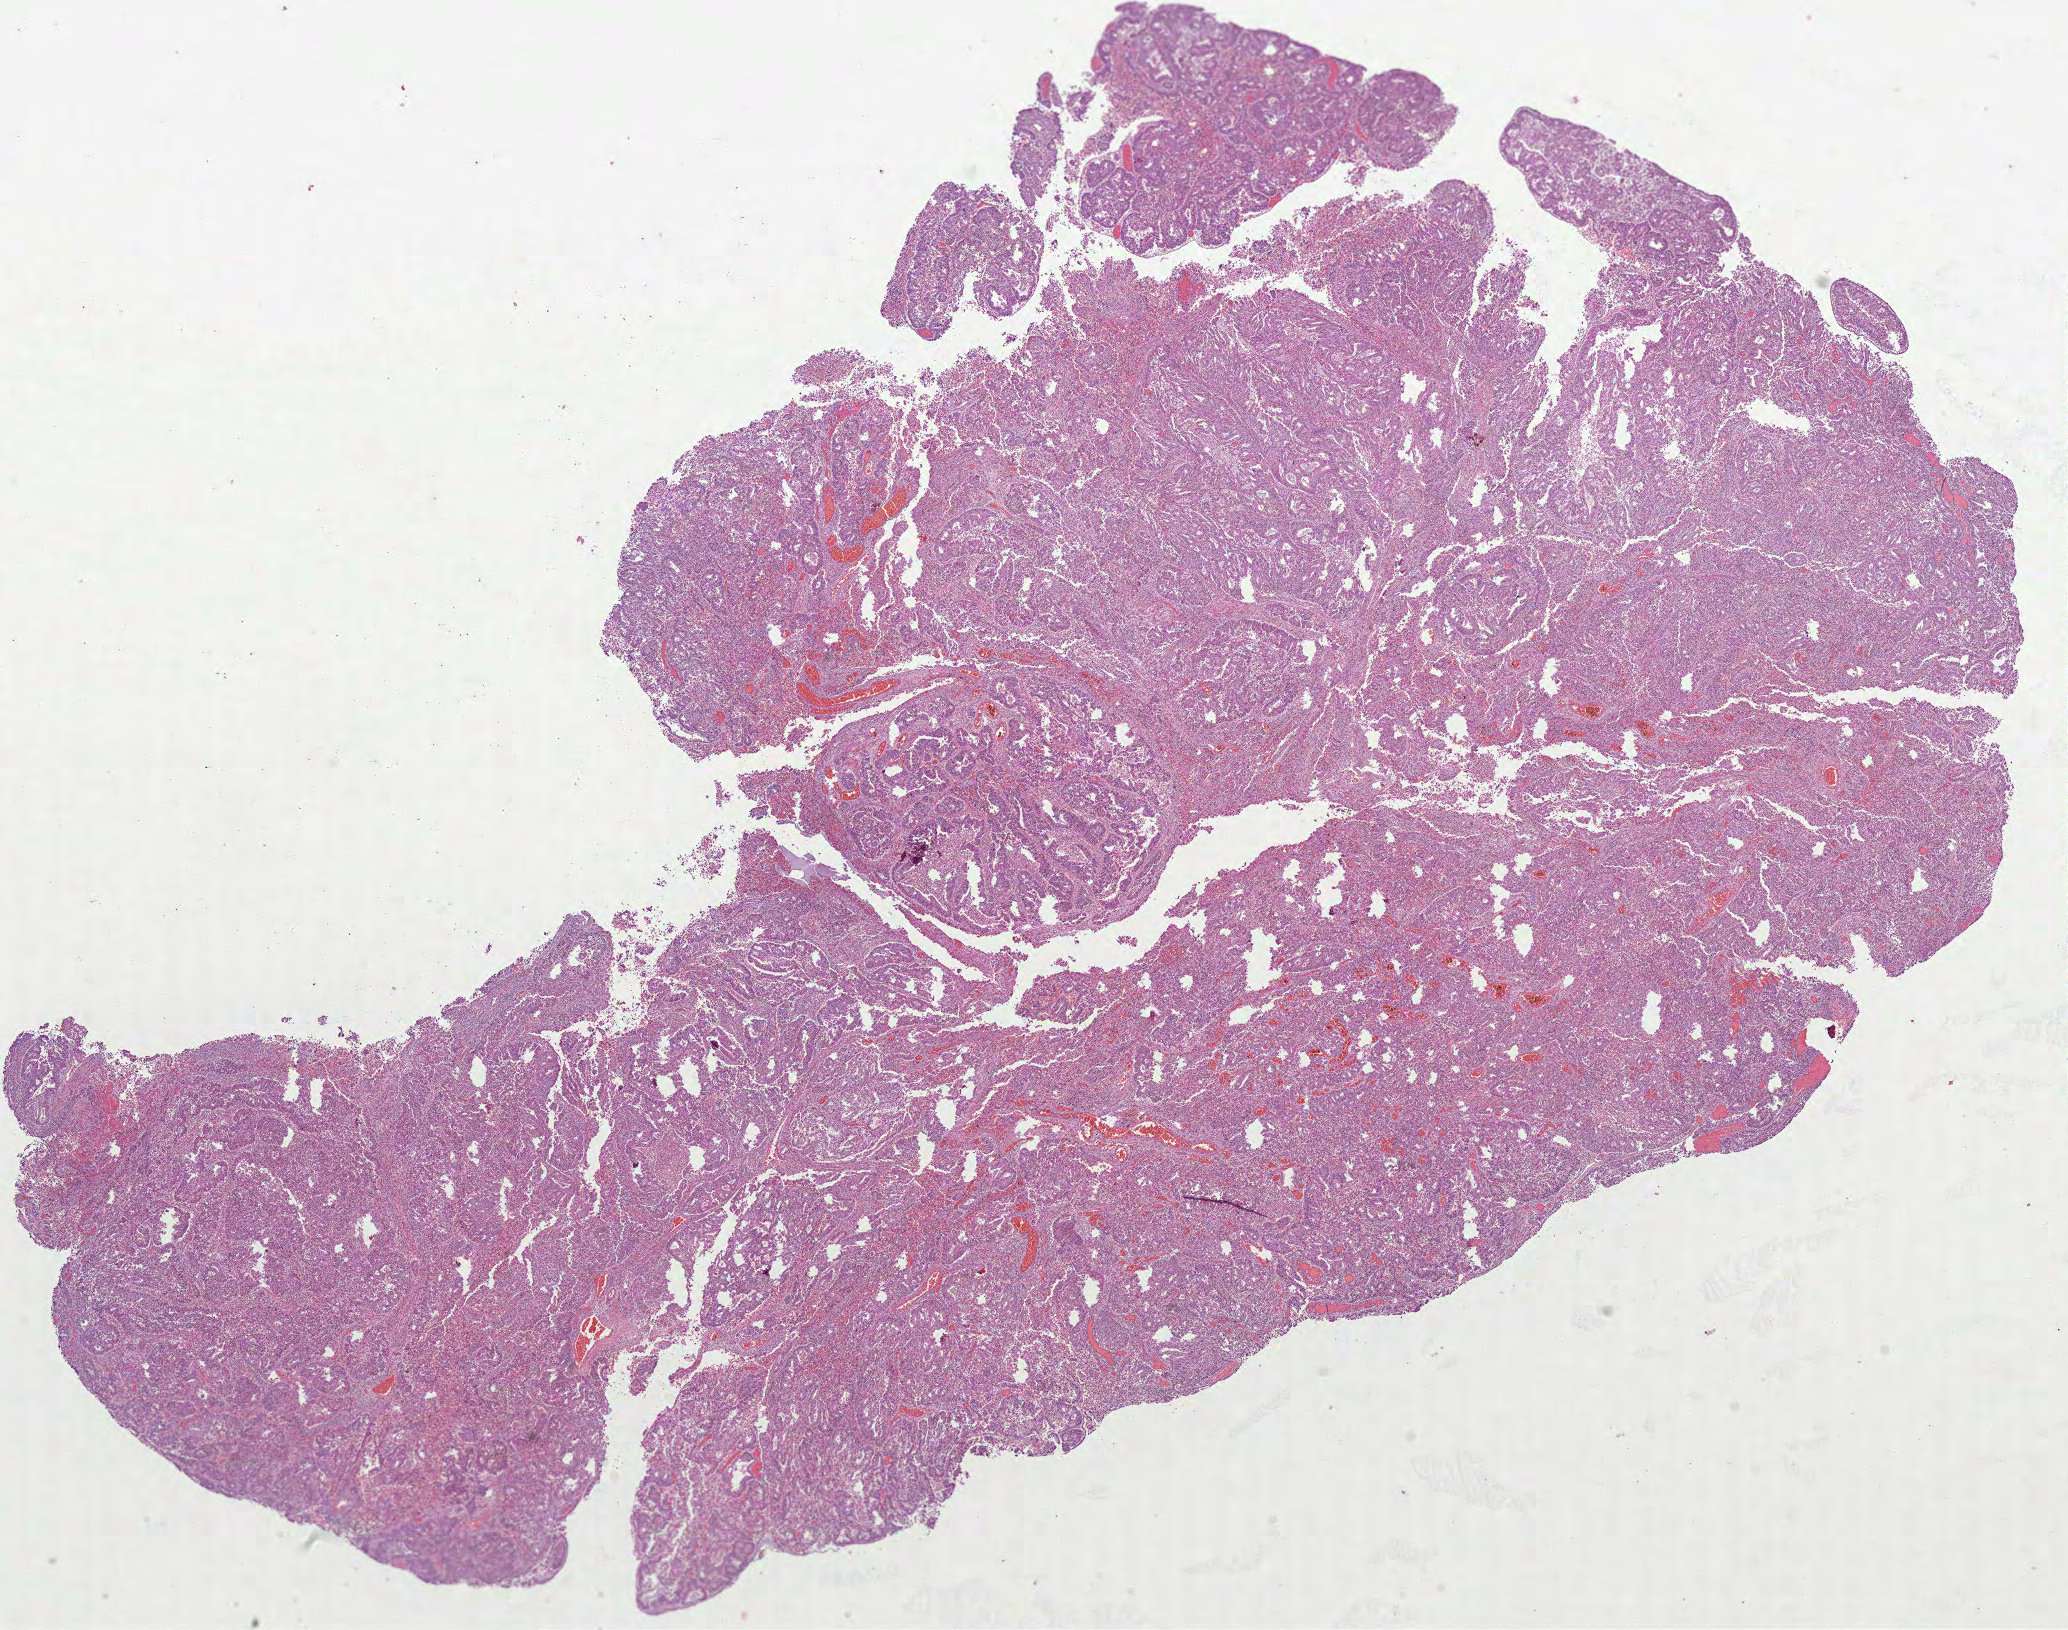
H&E whole-slide image, low-resolution overview of the scanned area, about 16.7 x 13.1 mm, formalin-fixed paraffin-embedded (FFPE) diagnostic section, uterus, primary tumour sample. Female patient; age at initial diagnosis 67 years.
Pathologic diagnosis: Endometrioid adenocarcinoma, NOS (endometrium).